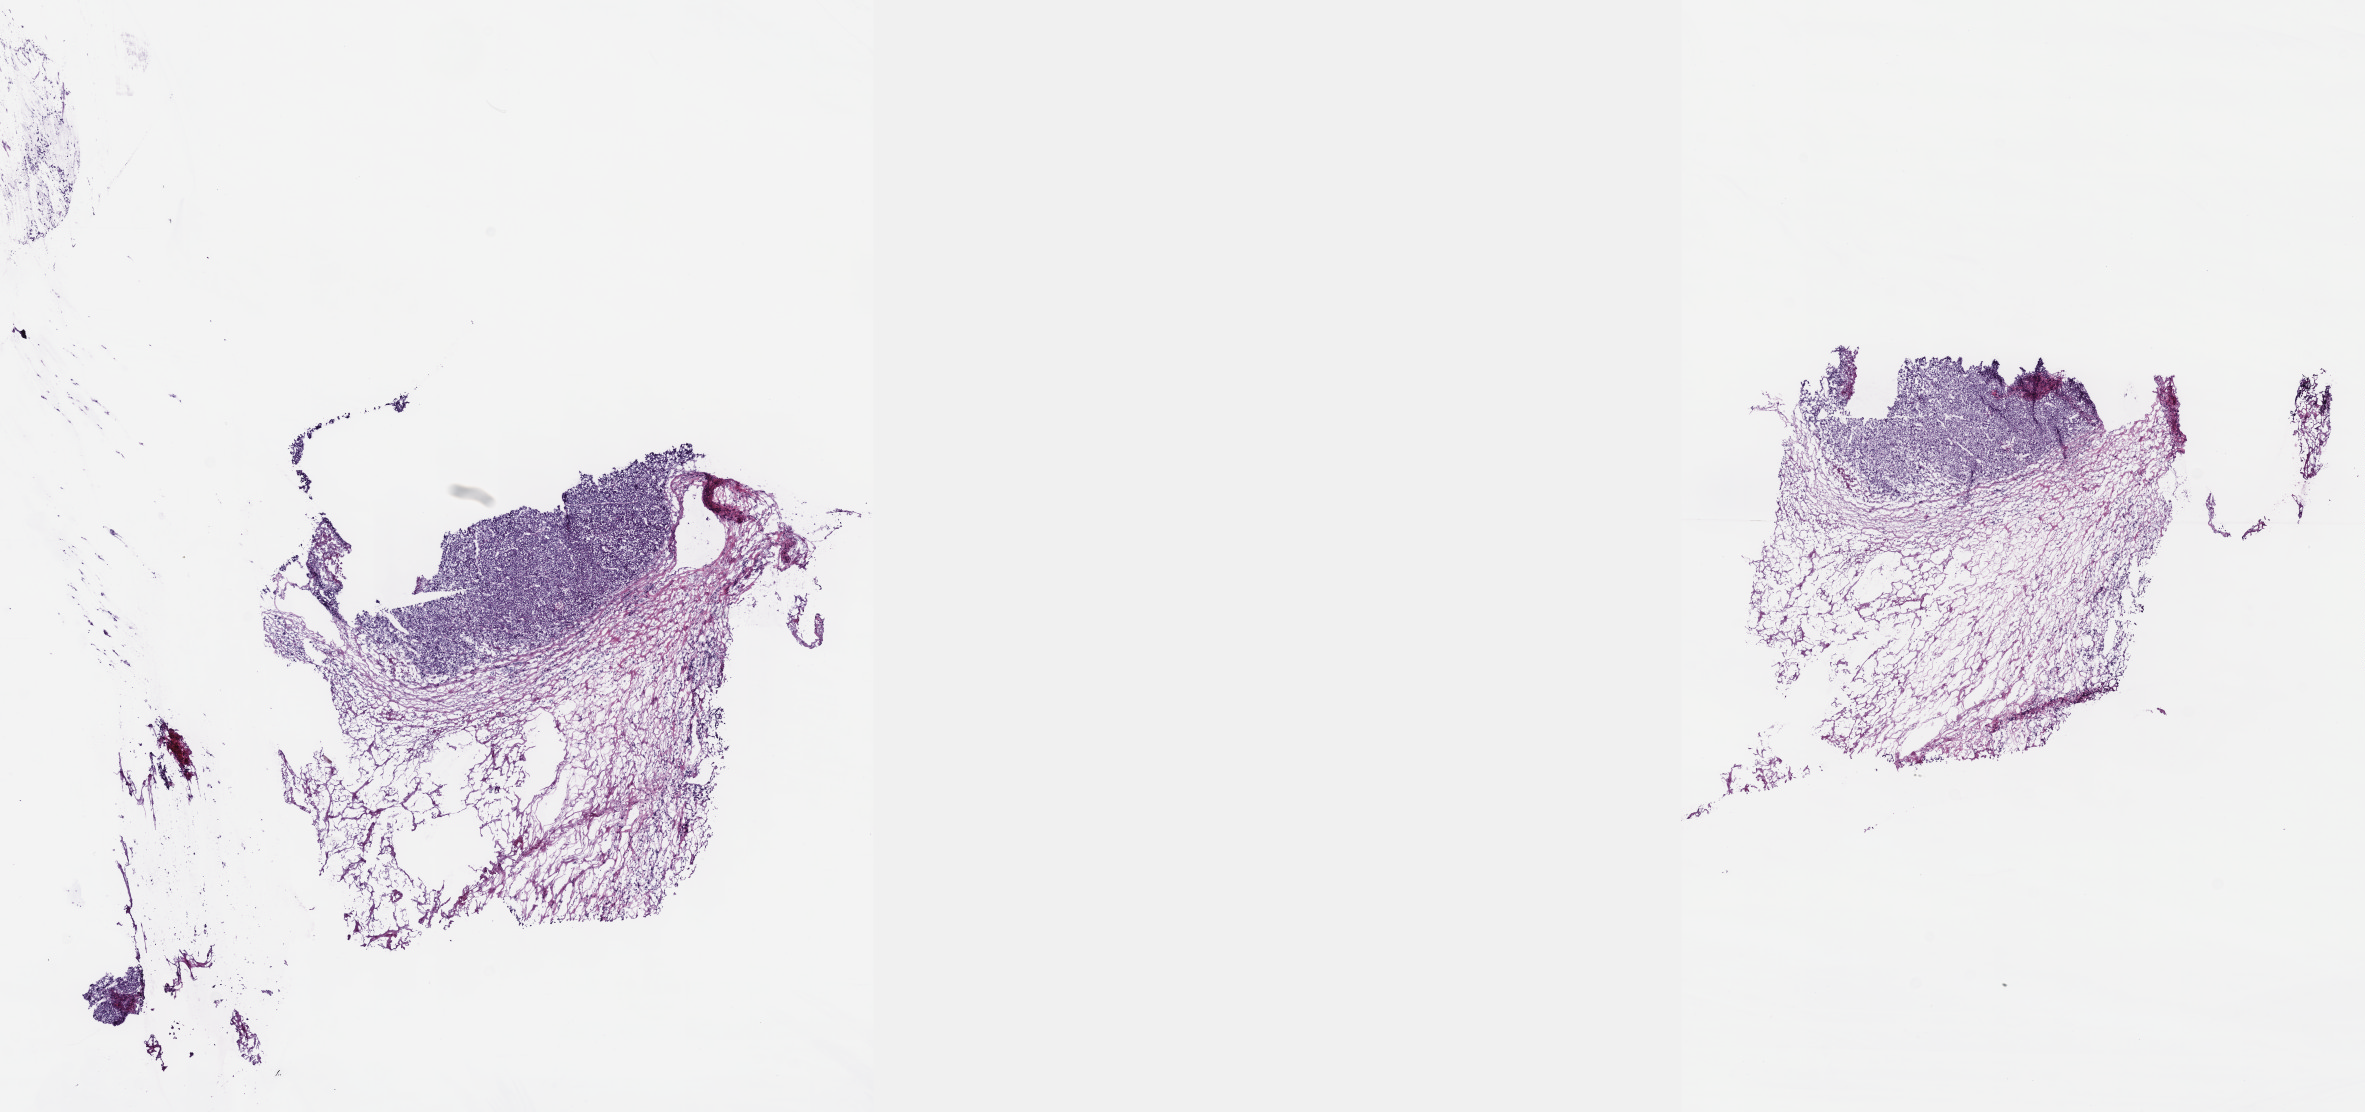
Hematoxylin and eosin (H&E) stained whole-slide image, low-resolution overview of the scanned area, about 19.1 x 9.0 mm (from a 40x scan), frozen section from the top of the tissue portion, liver, primary tumour sample. Patient: female, age at initial diagnosis 85 years.
Diagnosis: Hepatocellular carcinoma, NOS.